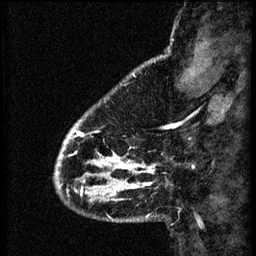
Breast MRI (dynamic contrast-enhanced), one sagittal slice; position 11 of 60 along the scan axis; 3 images stored at this slice position (order not interpretable as contrast timing); 1.5 T; TE 4.2 ms, TR 8.2 ms; 2.2 mm slice thickness; 256 × 256 image matrix. Patient: female, 41 years.
Annotated regions visible in this slice (semi-automatically segmented with operator editing):
- analysis volume of interest (the breast-tissue region the enhancement analysis was run in; not a lesion): bounding box [x1, y1, x2, y2] px = [56, 106, 156, 205]
- tumour enhancement mask (voxels above the 70 % enhancement threshold inside the analysis volume of interest): [56, 122, 155, 201]